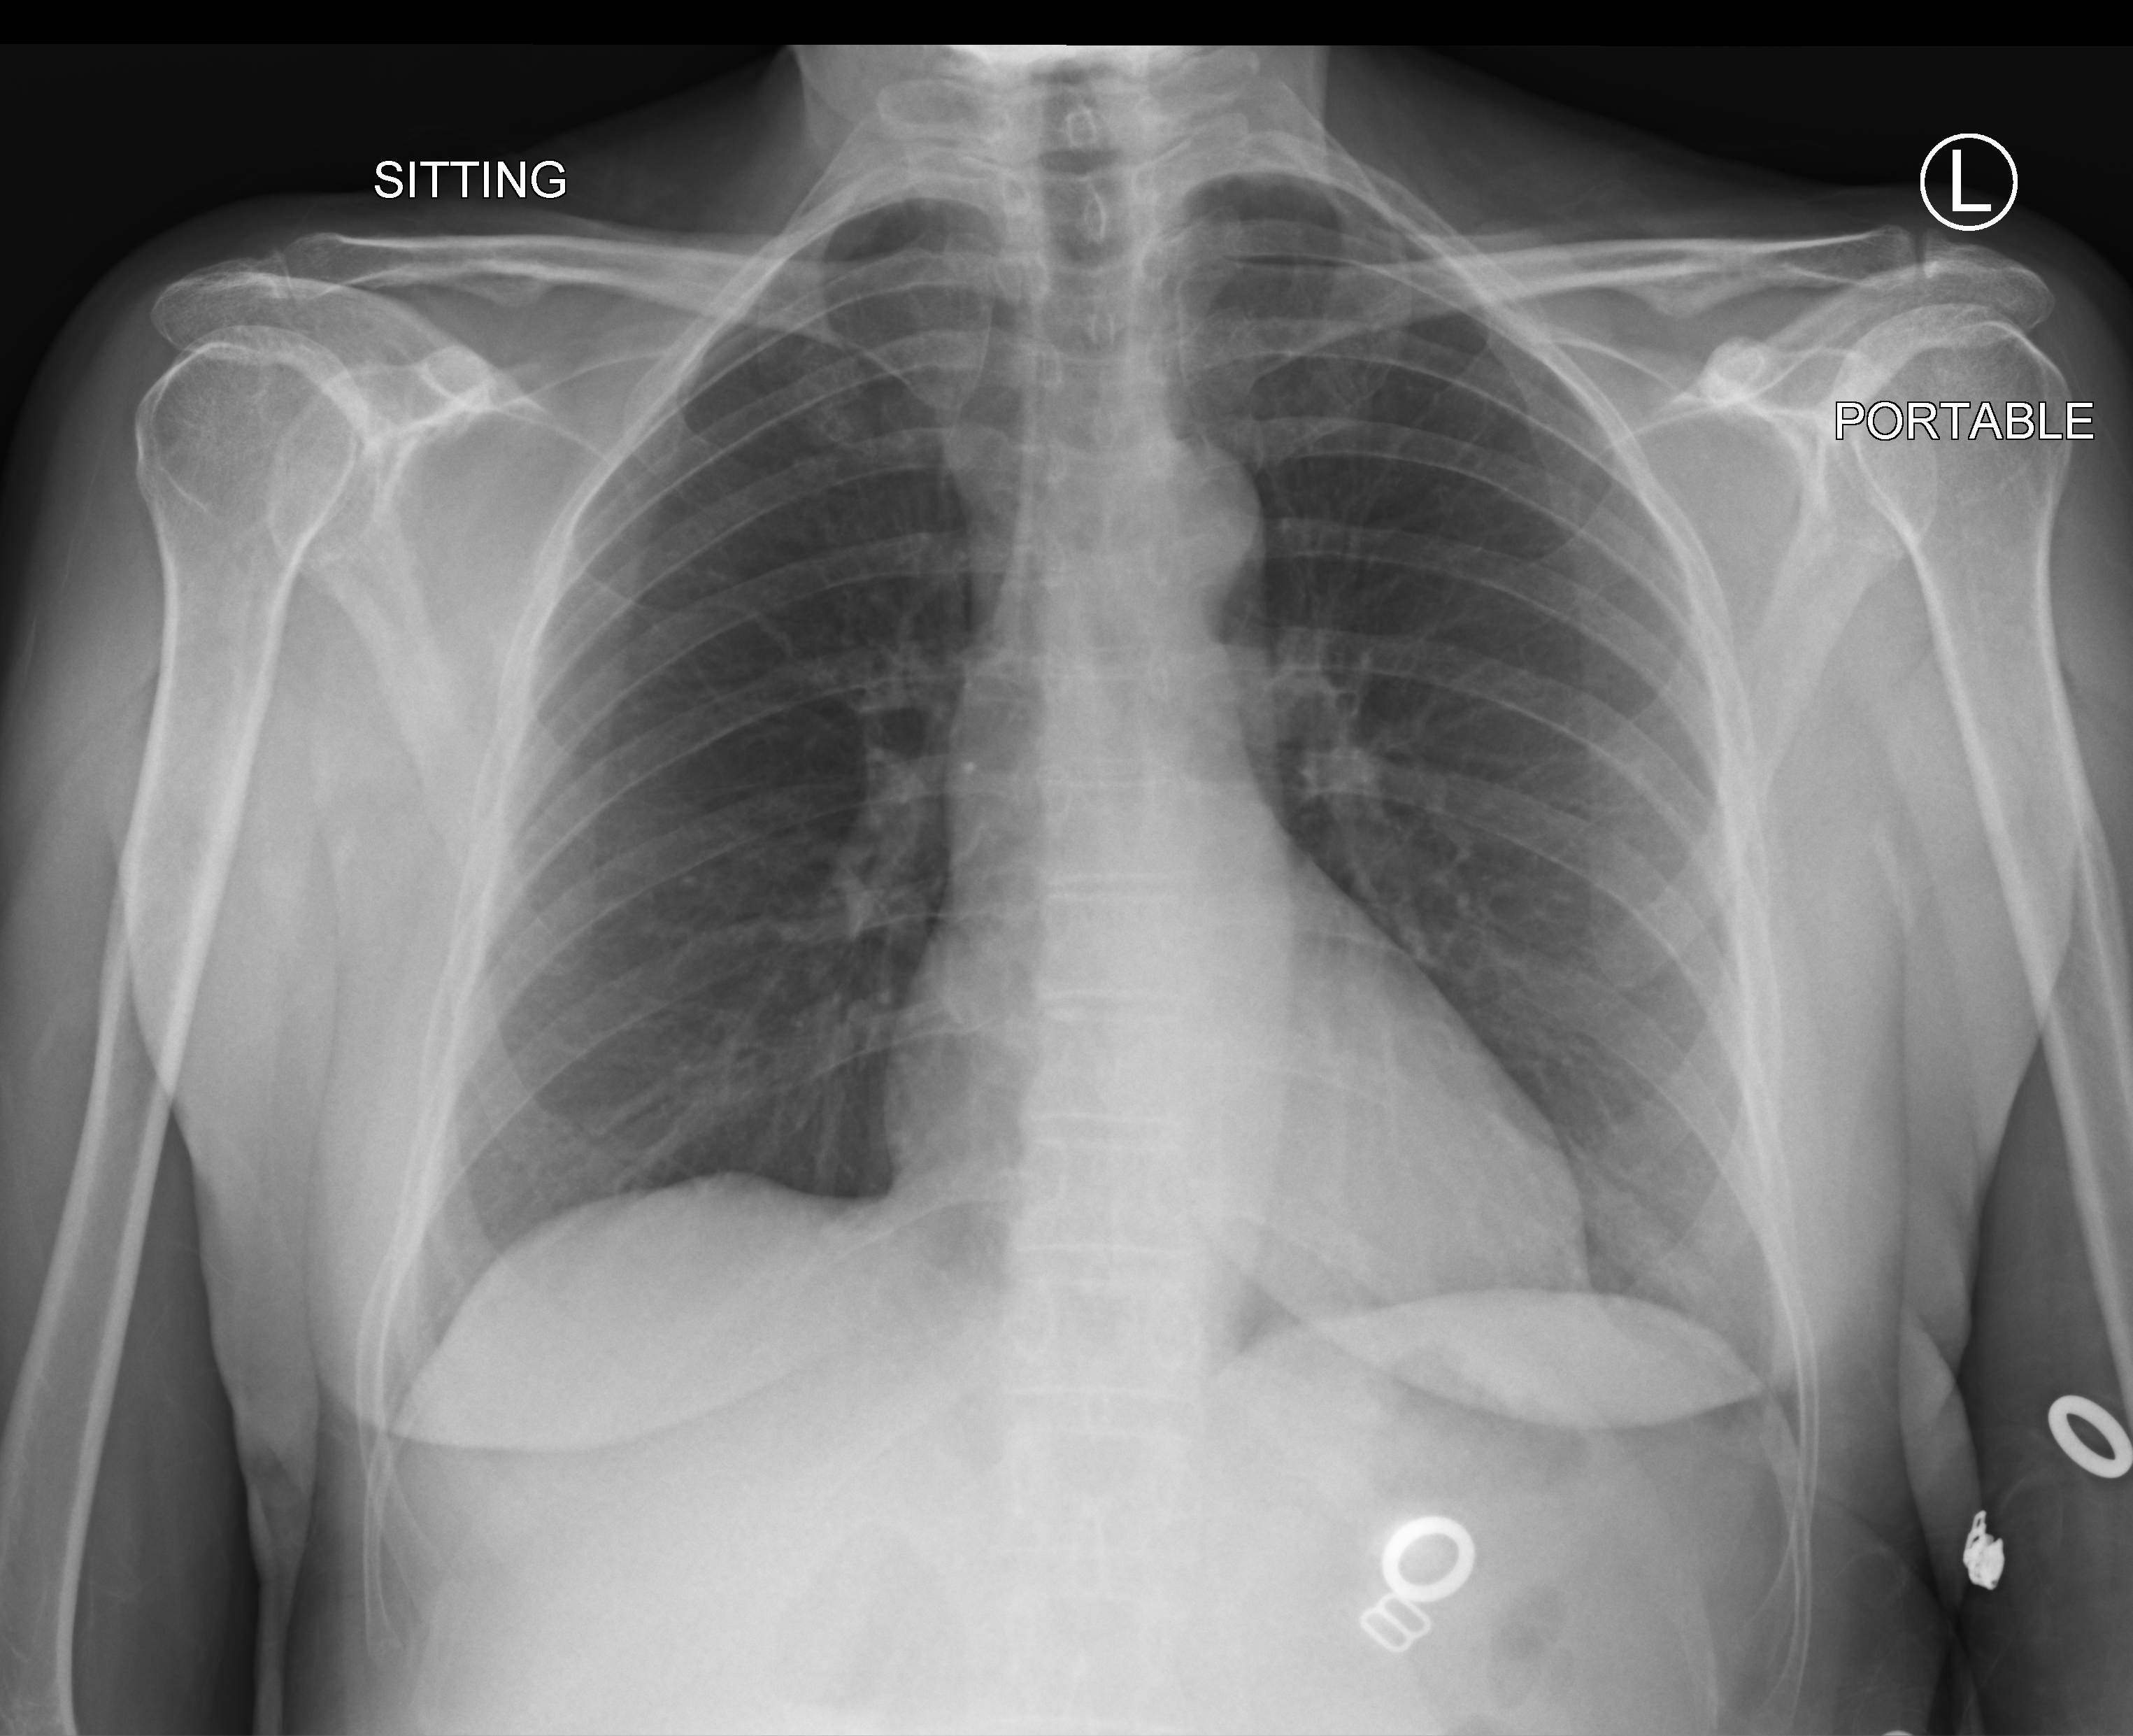
Chest X-ray (portable); anteroposterior (AP) projection. Female patient hospitalised with COVID-19, age 18–59 years.
Admission-level facts for this patient (not findings on this image; timing relative to this image not recorded):
- mechanically ventilated during this hospital stay: no